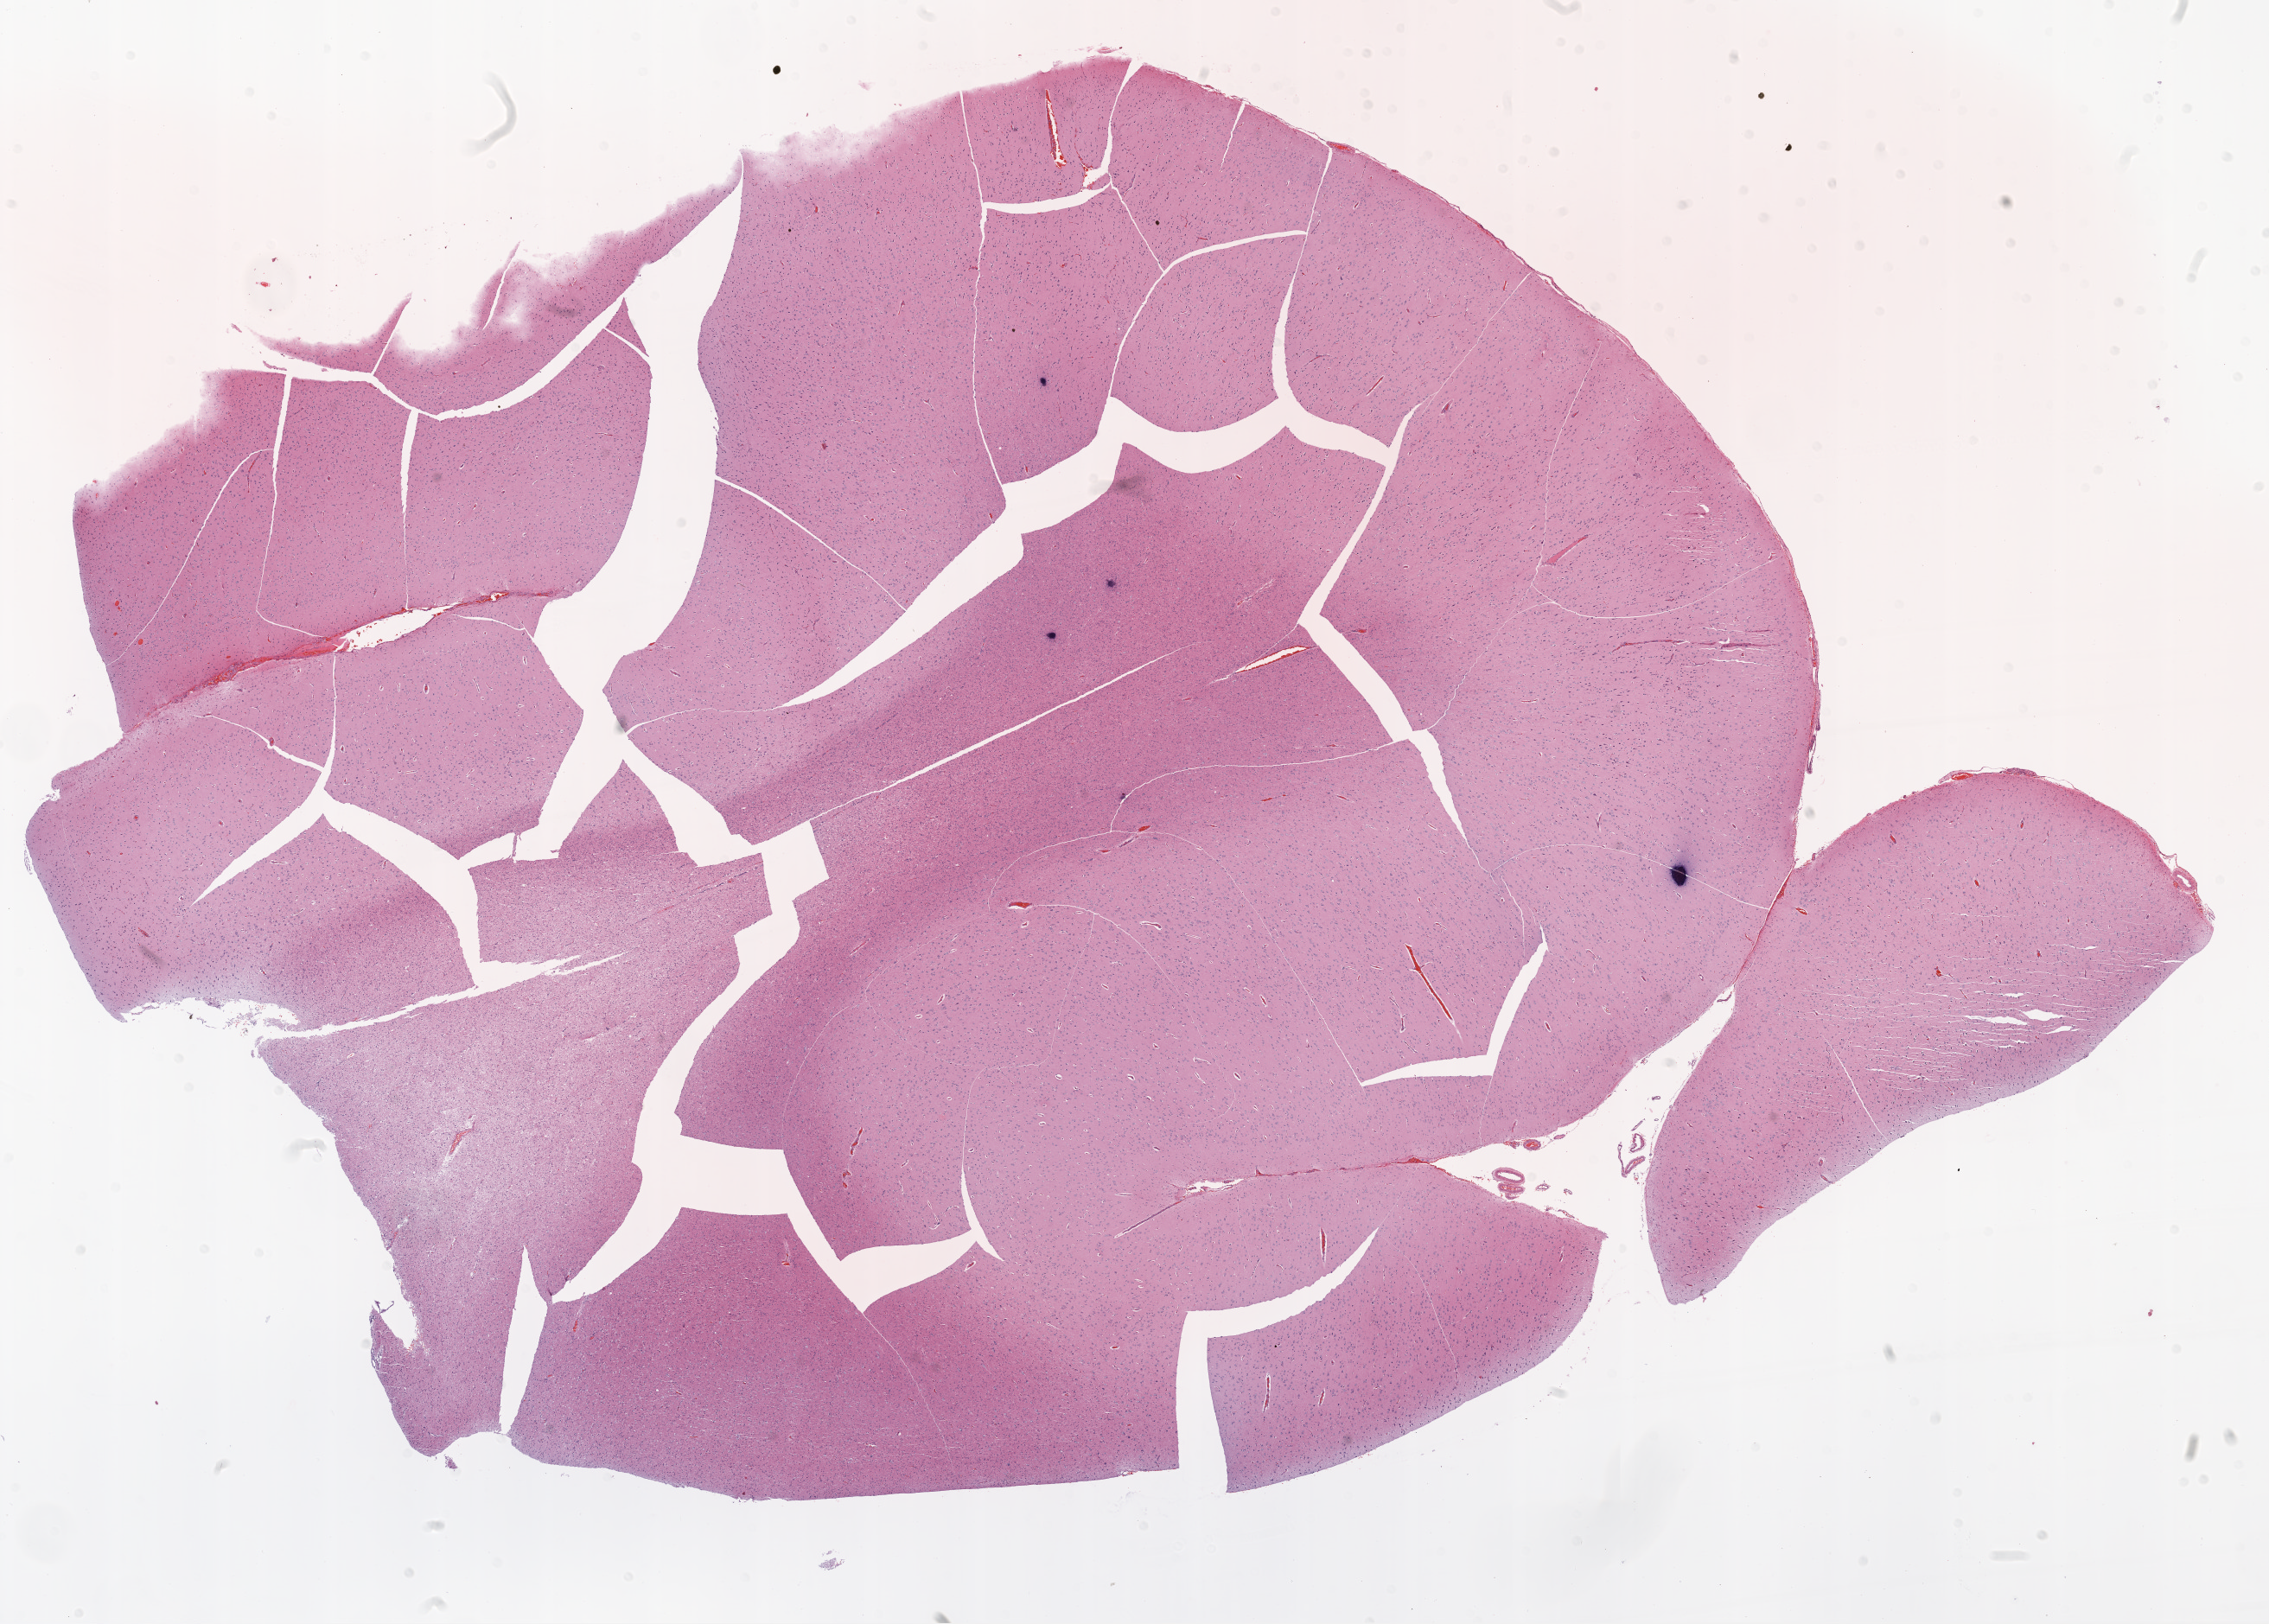
Whole-slide histology image, H&E-stained, shown as a low-resolution overview of the whole scanned area (about 21.1 x 15.1 mm). FFPE section. Primary tumour sample from the brain. Male patient; age at initial diagnosis 71 years.
Pathologic diagnosis: Glioblastoma.